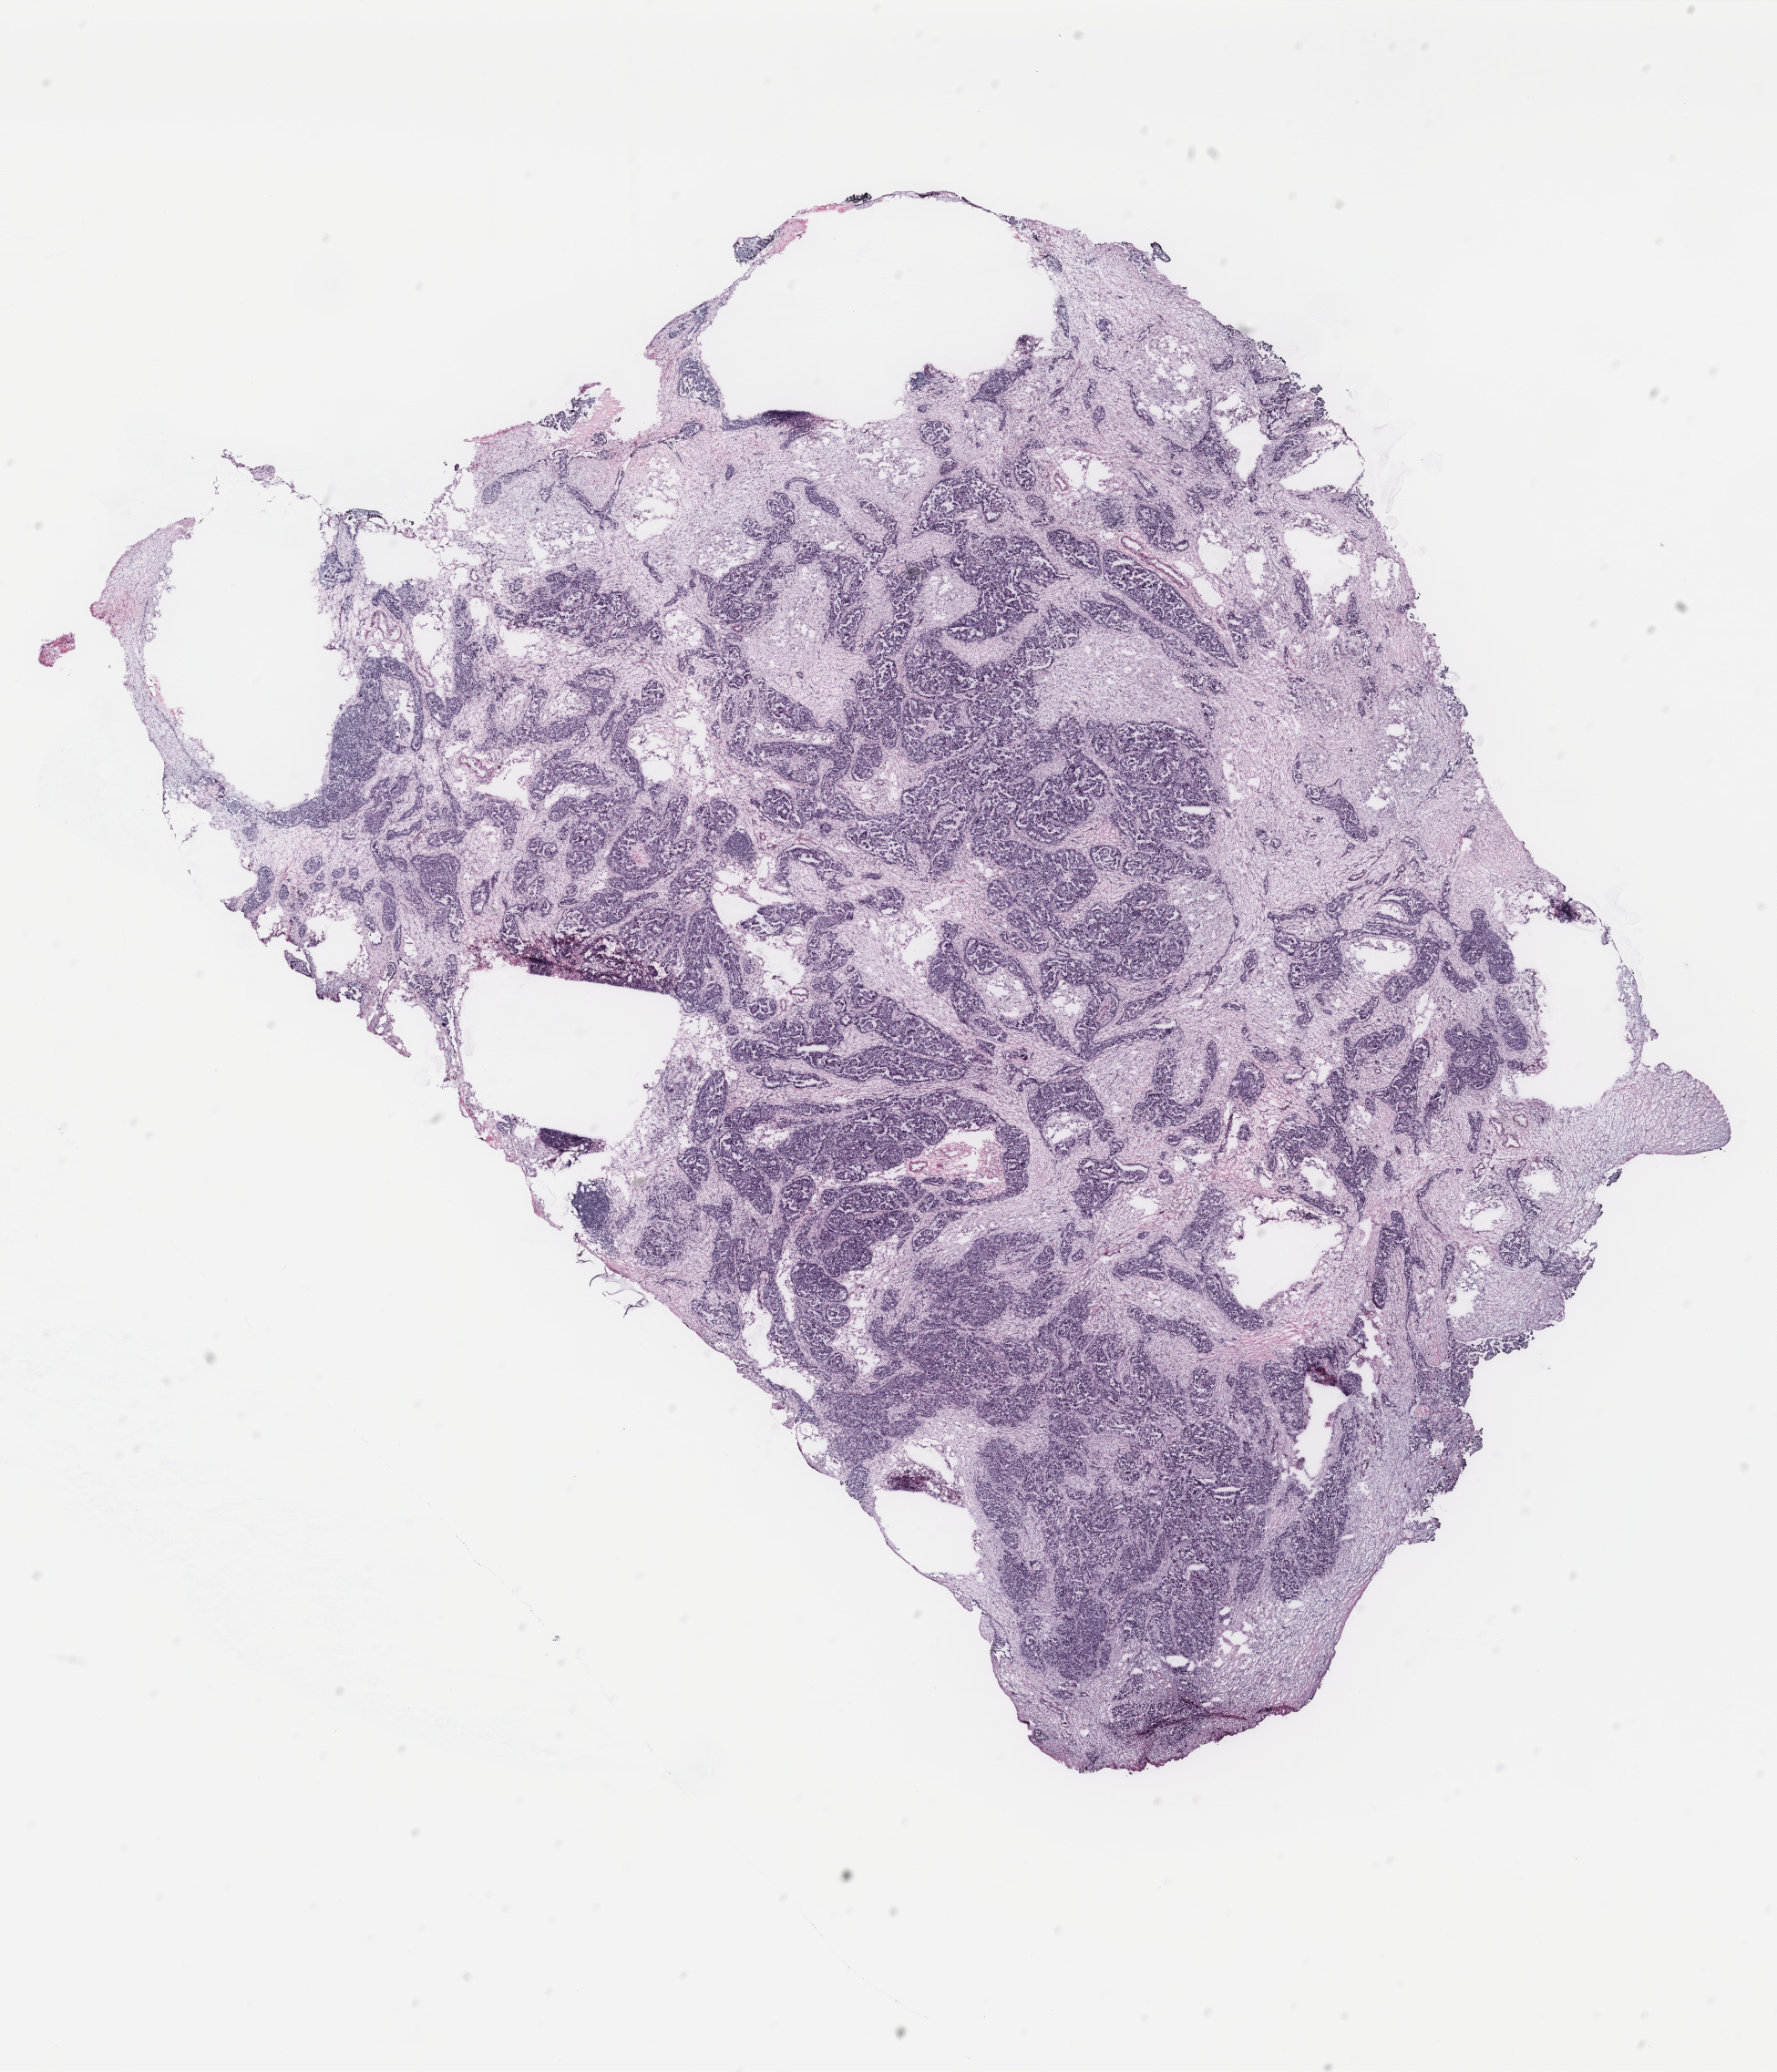
Digitized H&E-stained tissue section (whole slide) — a low-resolution overview of the entire scanned area, about 15.6 x 18.2 mm (from a 40x scan). Tumour tissue sample, ovary. 77-year-old female patient.
Primary tumour site (as recorded): peritoneum. Histologic diagnosis: Serous adenocarcinoma, NOS (peritoneum, NOS).